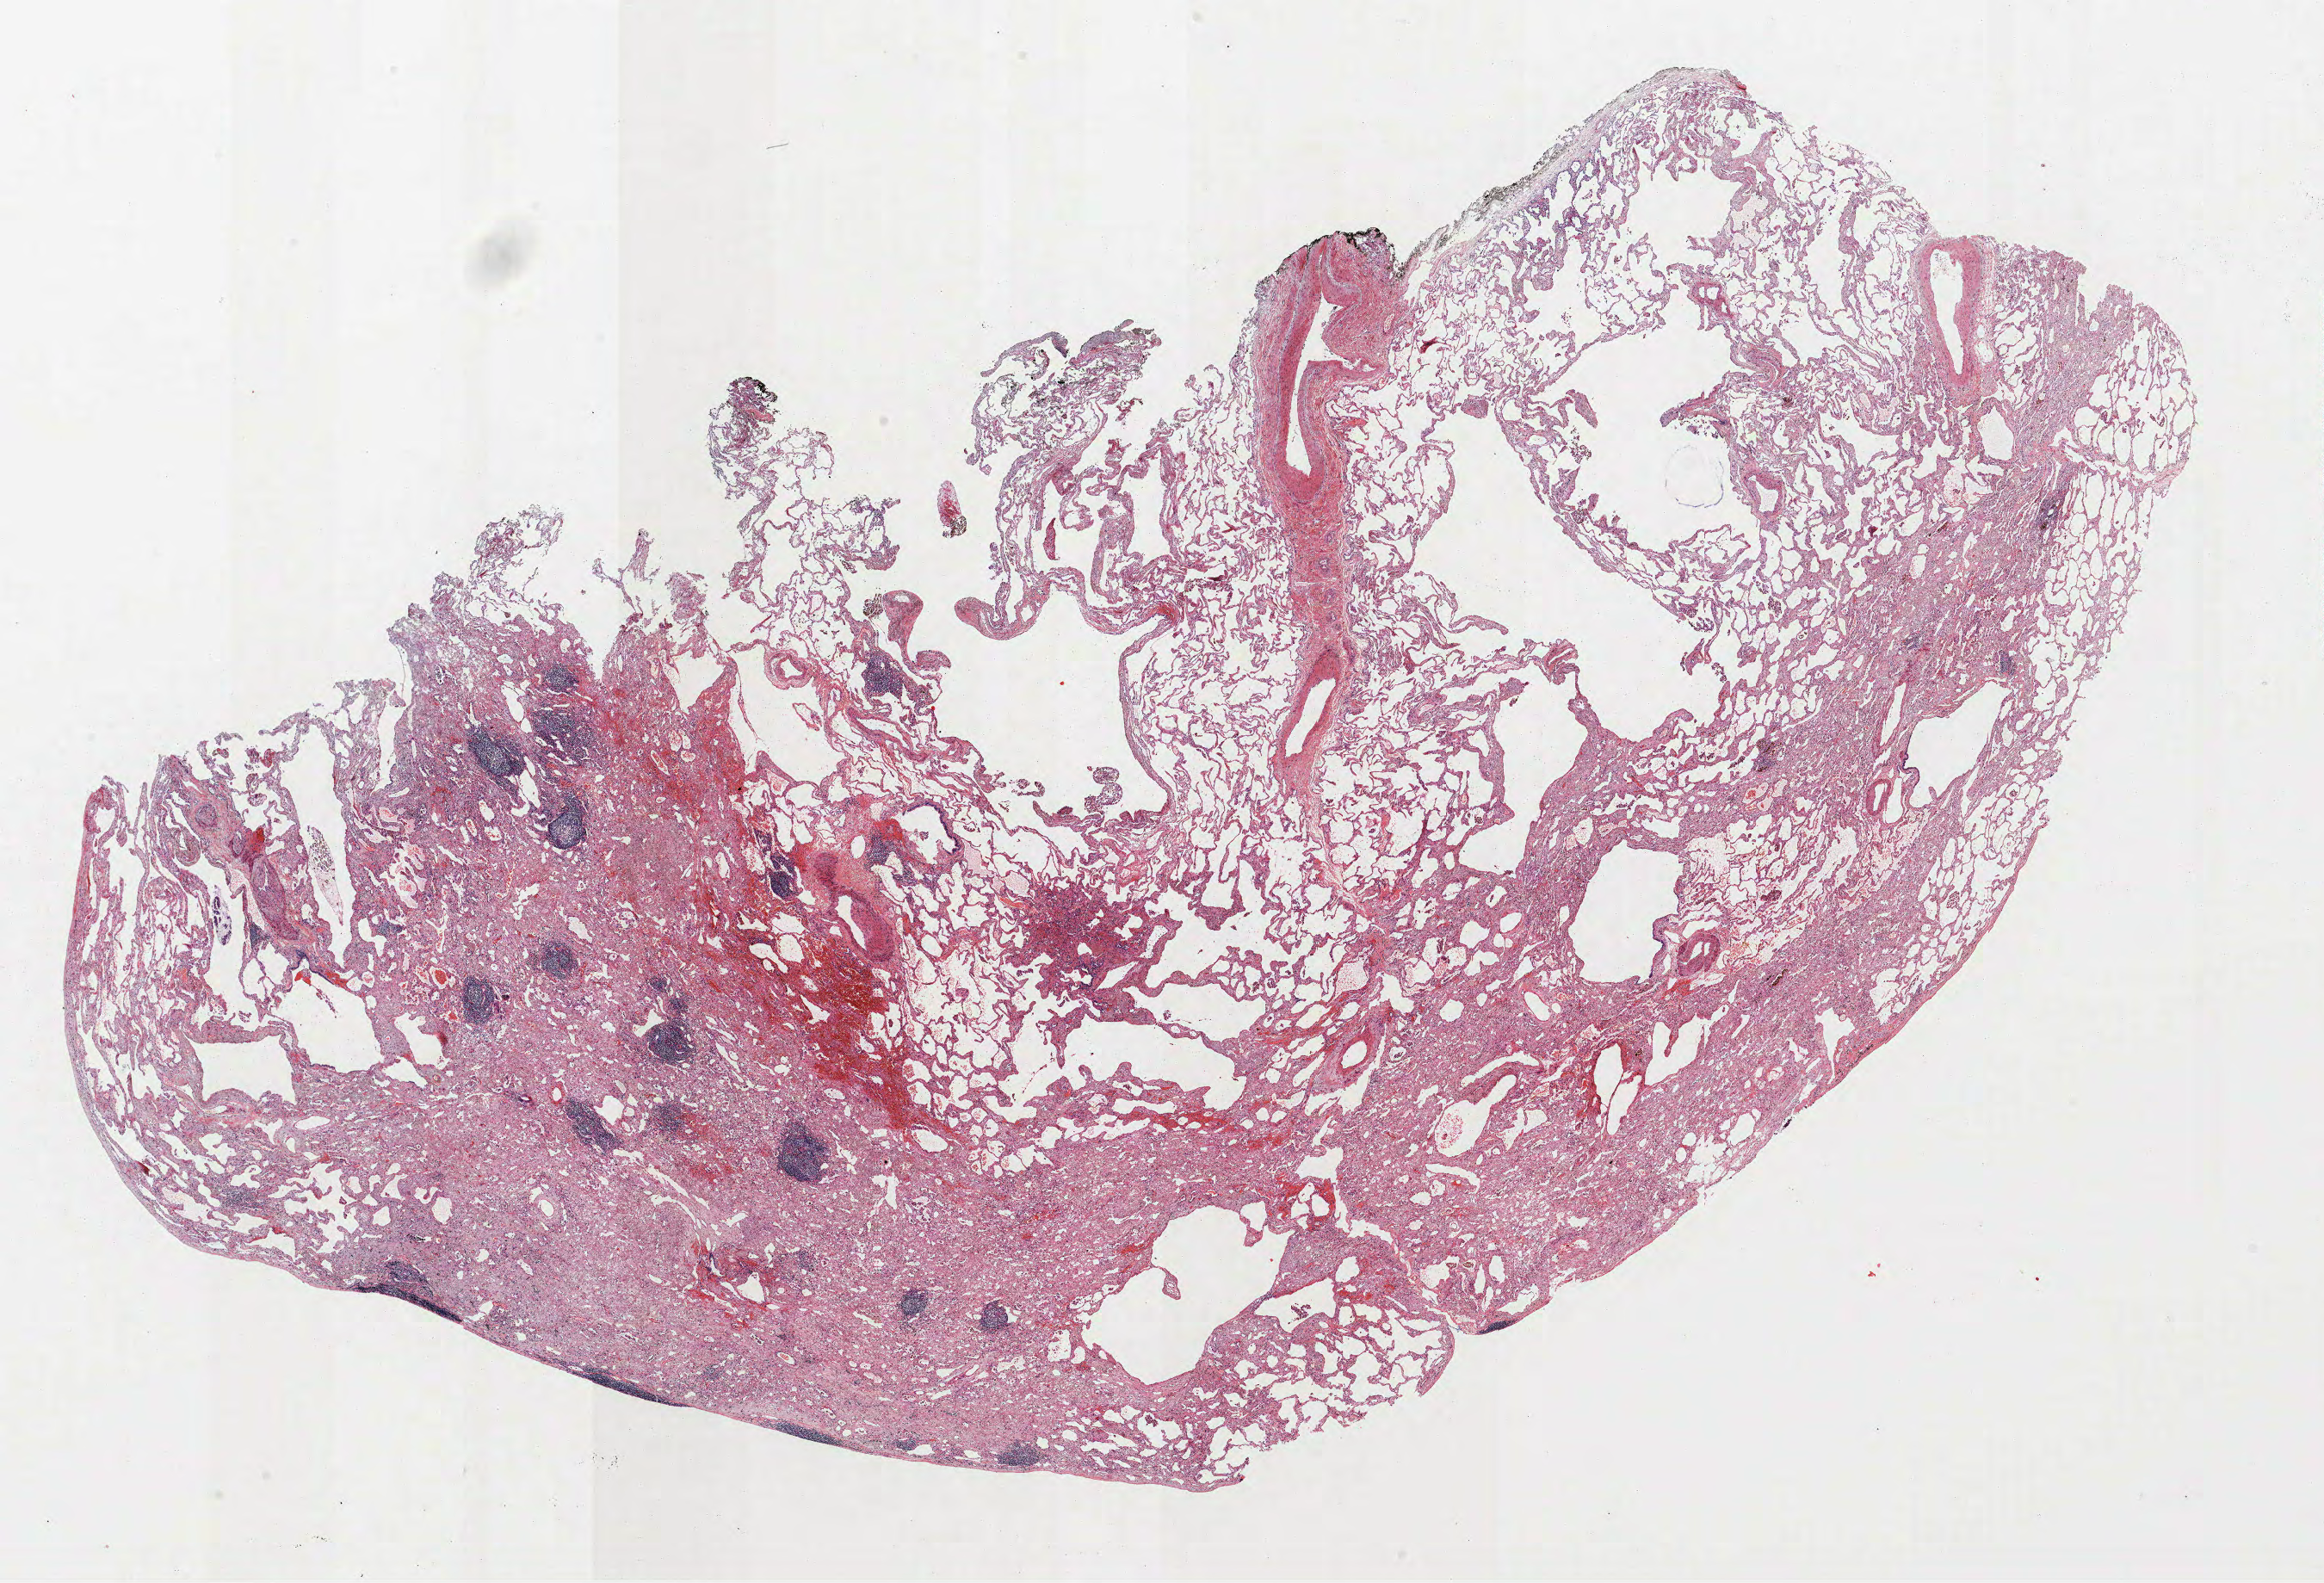
Whole-slide histology image, H&E-stained — a low-resolution overview of the entire scanned area, about 21.6 x 14.7 mm (slide scanned at 40x); formalin-fixed paraffin-embedded (FFPE) section; lung. Female, age 65 at enrolment. Current smoker at enrolment. Grade: moderately differentiated (G2).
- participant's lung-cancer diagnosis: Acinar cell carcinoma (ICD-O-3 8550/3)
- primary tumour location (clinical record): right upper lobe
- tumour size (pathology): 15 mm
- stage (AJCC 6th edition): IA